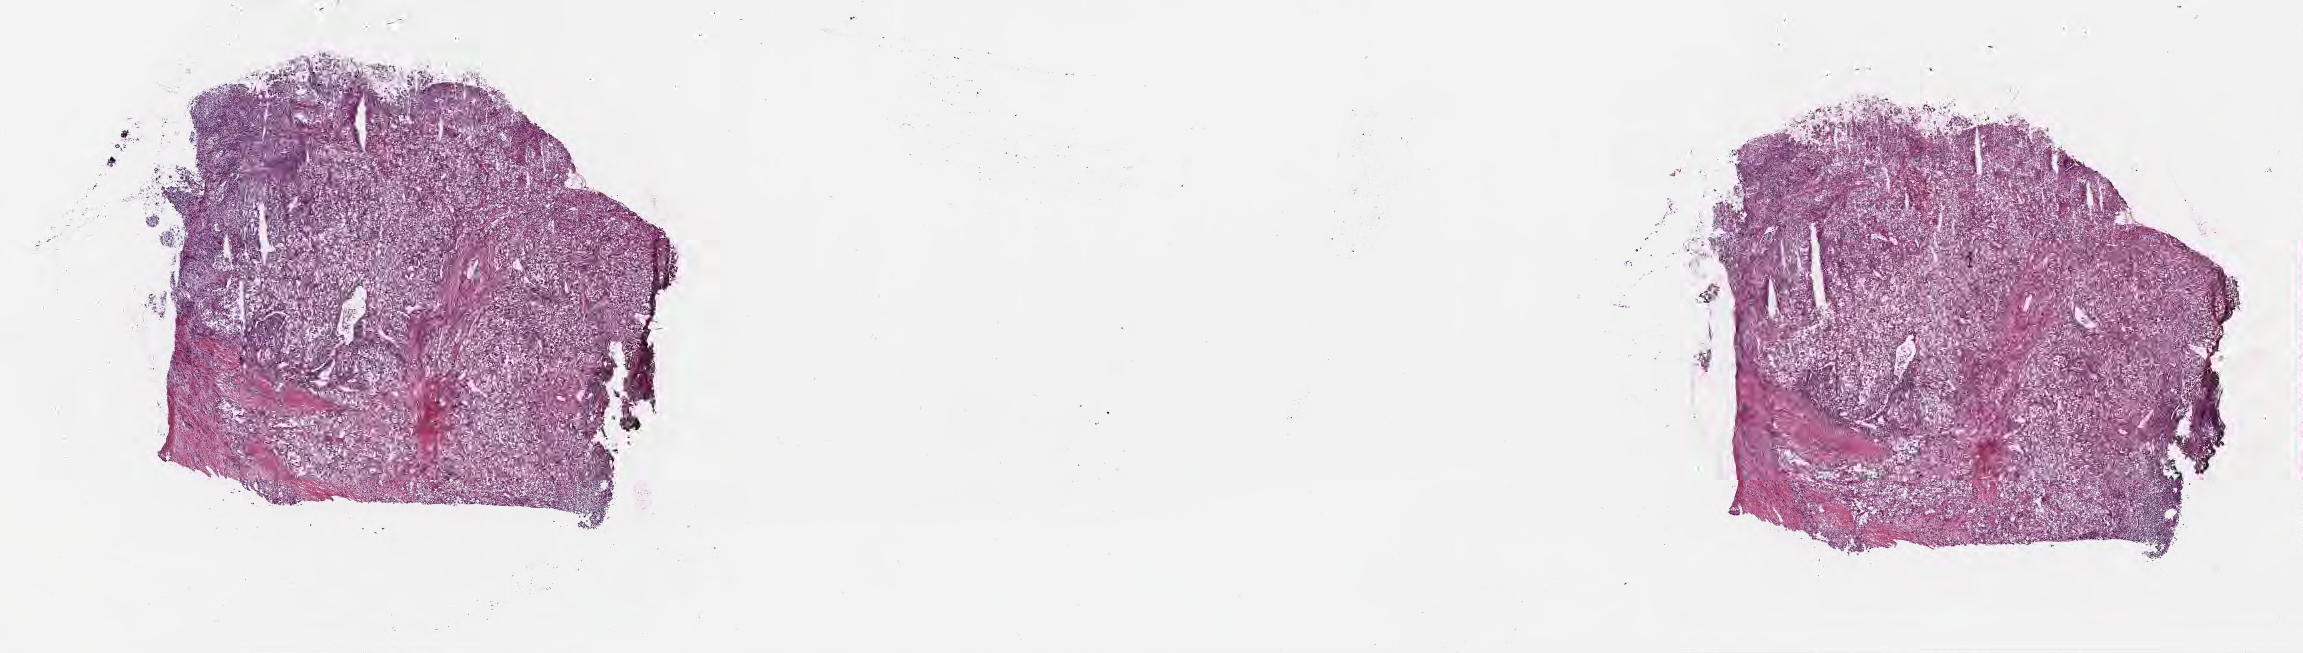
Whole-slide image, H&E stain — low-resolution overview of the scanned area, about 18.6 x 5.3 mm. Frozen section. Specimen: primary tumor. Site: upper lobe of right lung. Male patient, aged 57. Composition of this section per pathologist review: tumor cells 80%, tumor nuclei 80%, stromal cells 18%, necrosis 2%, normal cells 0%. Infiltration values recorded for this section: lymphocyte infiltration 4%, monocyte infiltration 3%, neutrophil infiltration 4%.
AJCC pathologic stage: Stage IIA. Diagnosis: Solid carcinoma, NOS.